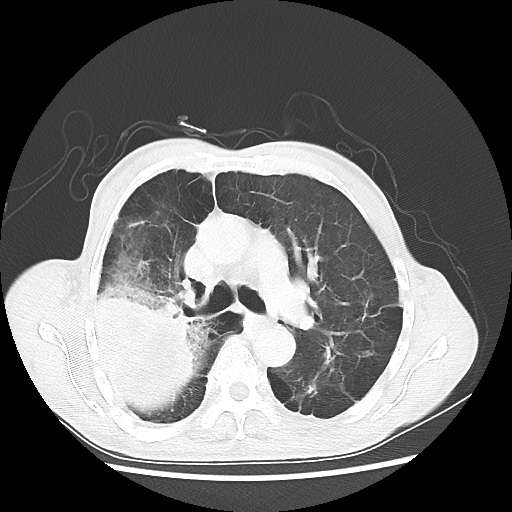
Chest CT, one axial slice; slice 34 of 58 in the series (ordered by position); reconstruction kernel LUNG; 100 kVp; lung window (W 1500 / L -600 HU); 5 mm slice thickness; 512 × 512 image matrix, field of view 351 × 351 mm. Male patient, age 75 years. From the clinical record (not read from this slice): clinical TNM (as recorded): T4 N1 M1.
Outlined on this slice (rectangle marked by the reading radiologist):
- lung tumour (recorded histology: adenocarcinoma): bounding box [x1, y1, x2, y2] px = [90, 283, 209, 419]